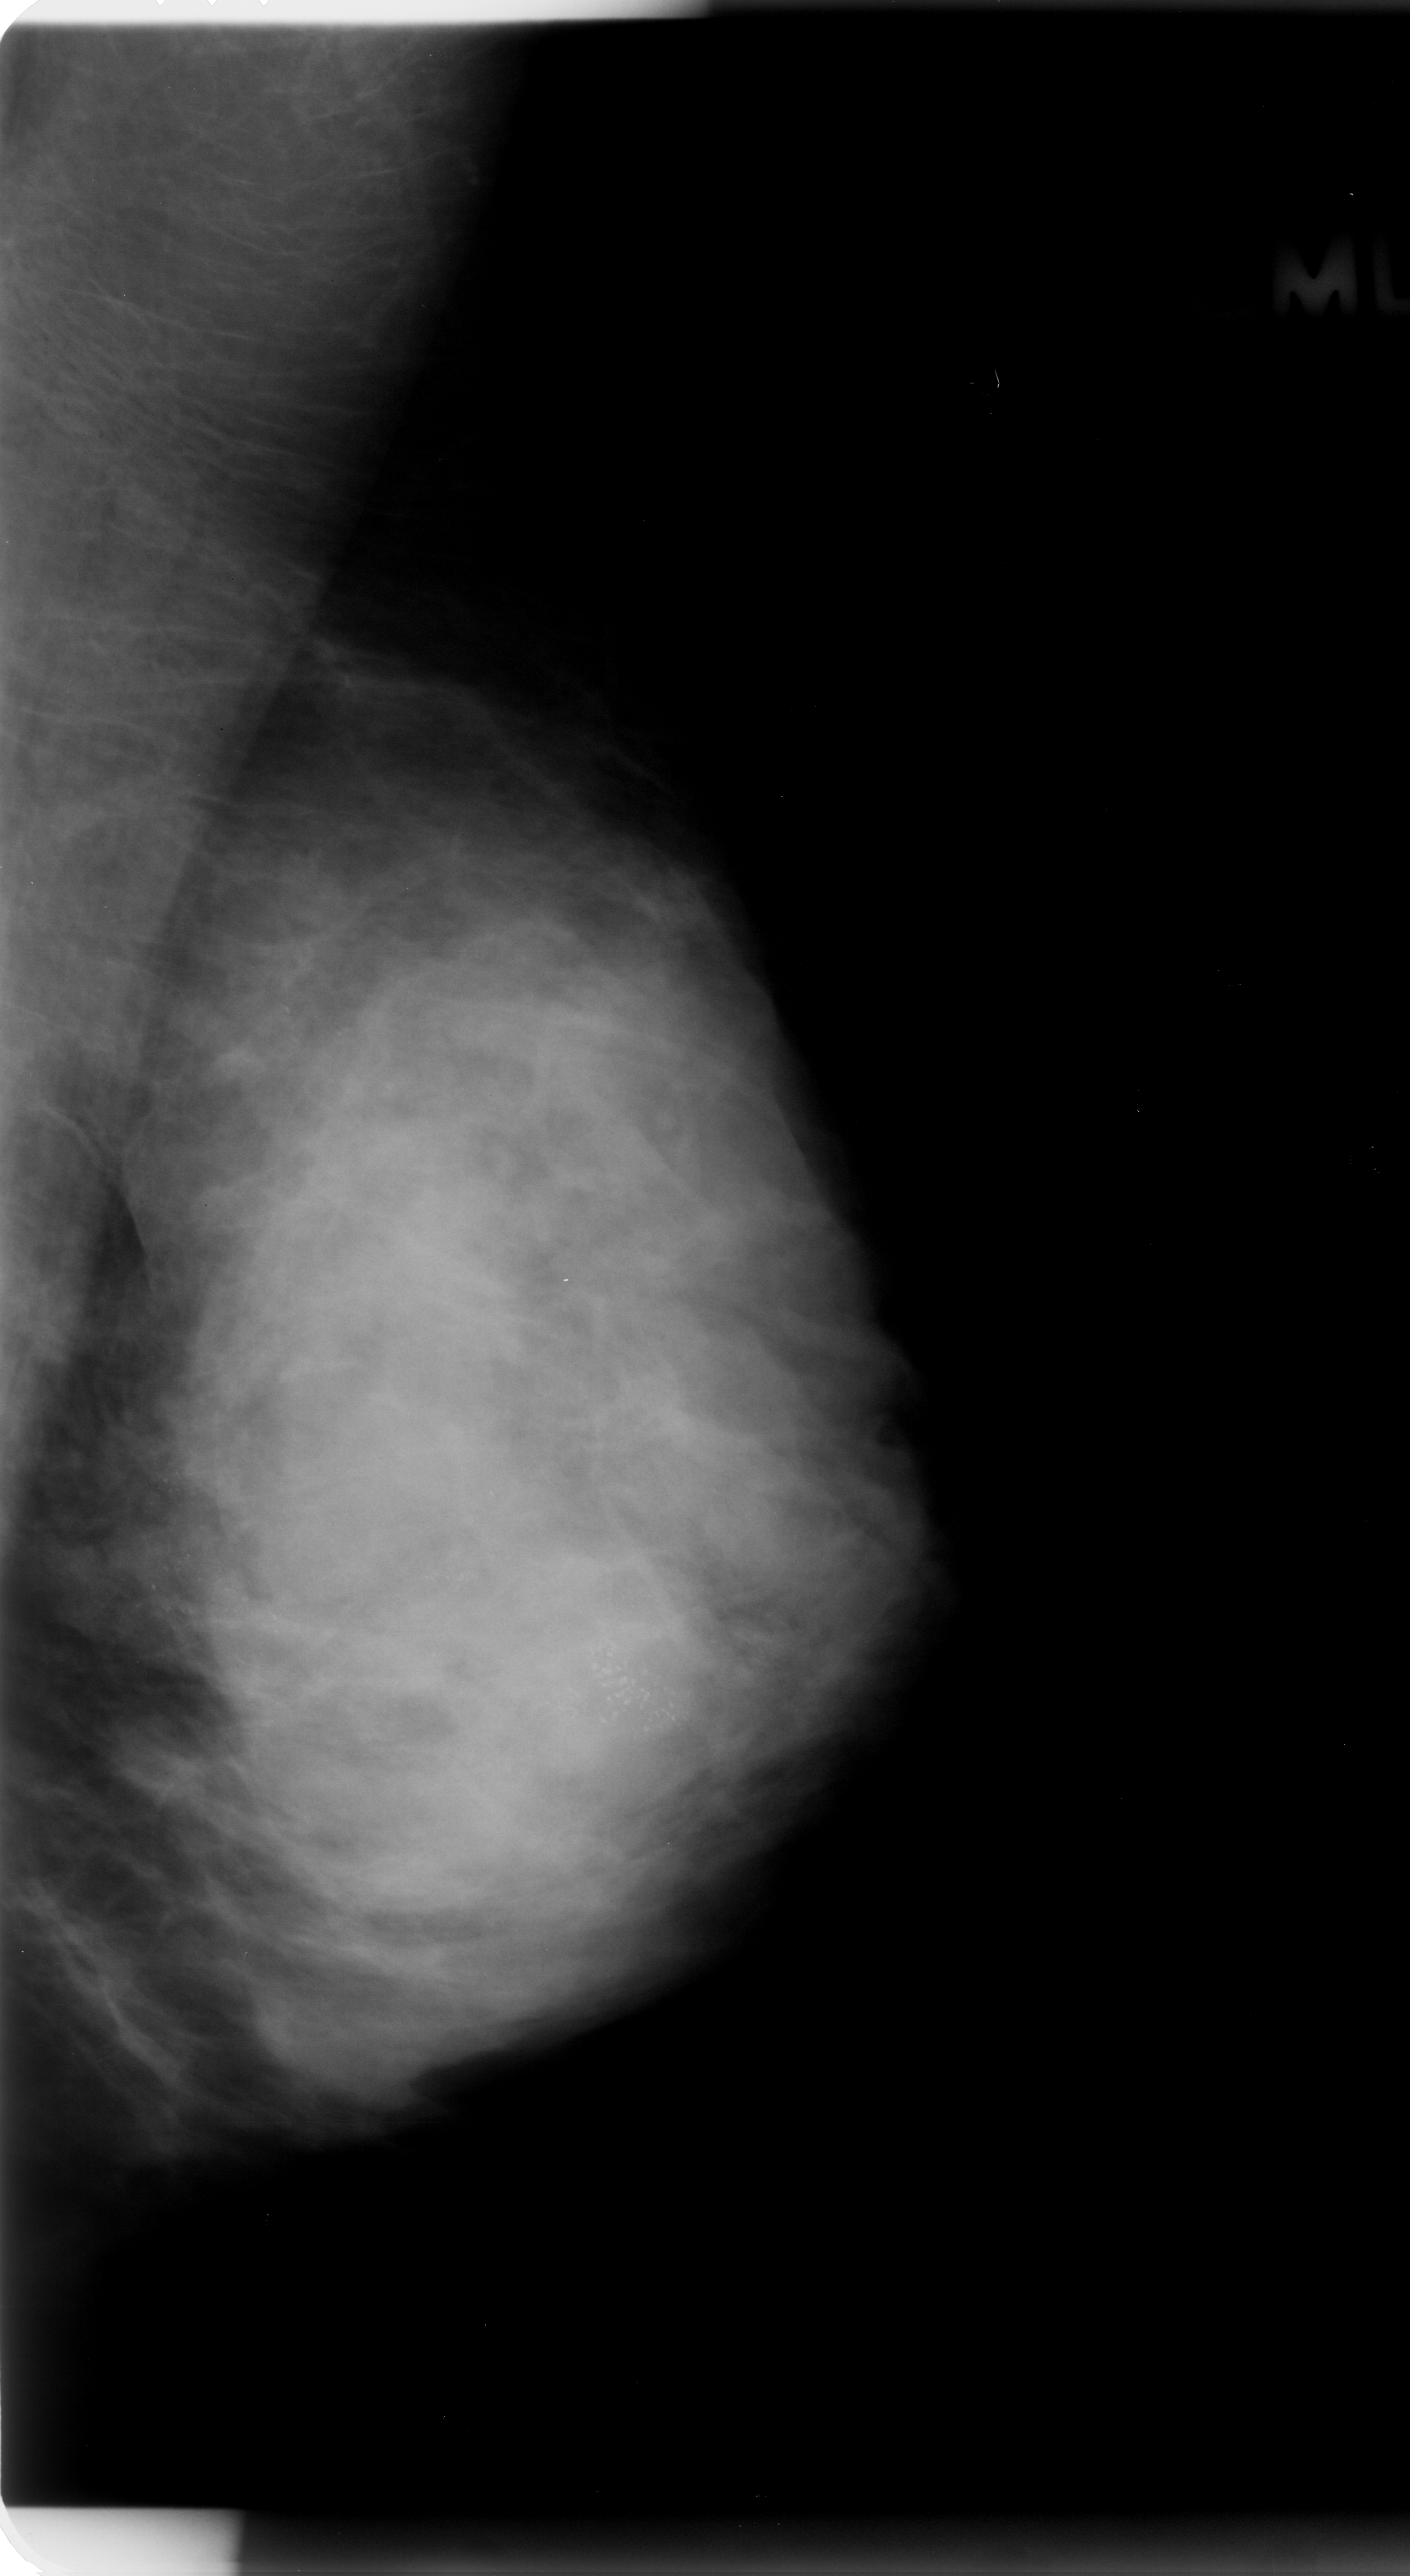
Scanned film-screen mammogram; left breast; MLO view; BI-RADS breast density category 4 (scale 1–4); 1410 × 2576 image matrix.
Expert-marked regions of interest on this film, with their recorded descriptors:
- calcifications, morphology amorphous / pleomorphic, distribution segmental; BI-RADS assessment category 5; pathology result (as recorded, not read from the image): malignant: bounding box (x1, y1, x2, y2) in pixels: (68, 1474, 807, 1827)